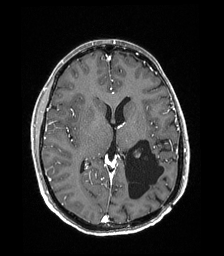
Brain MRI from a brain-tumour surgery series, one axial slice. Slice 93 of 192 in the series (ordered by position). T1-weighted post-contrast. 1 mm slice thickness. 224 × 256 image matrix. Case-level facts recorded for this patient, not image findings: histopathology: Low grade glioma; IDH mutation: no; tumour location: Left Parieto-Occipital Intraventricular.
Structures marked on this image (expert manual segmentation):
- previous resection cavity: bounding box <125,139,164,199> (left, top, right, bottom; pixels)
- tumour: <133,148,143,158>